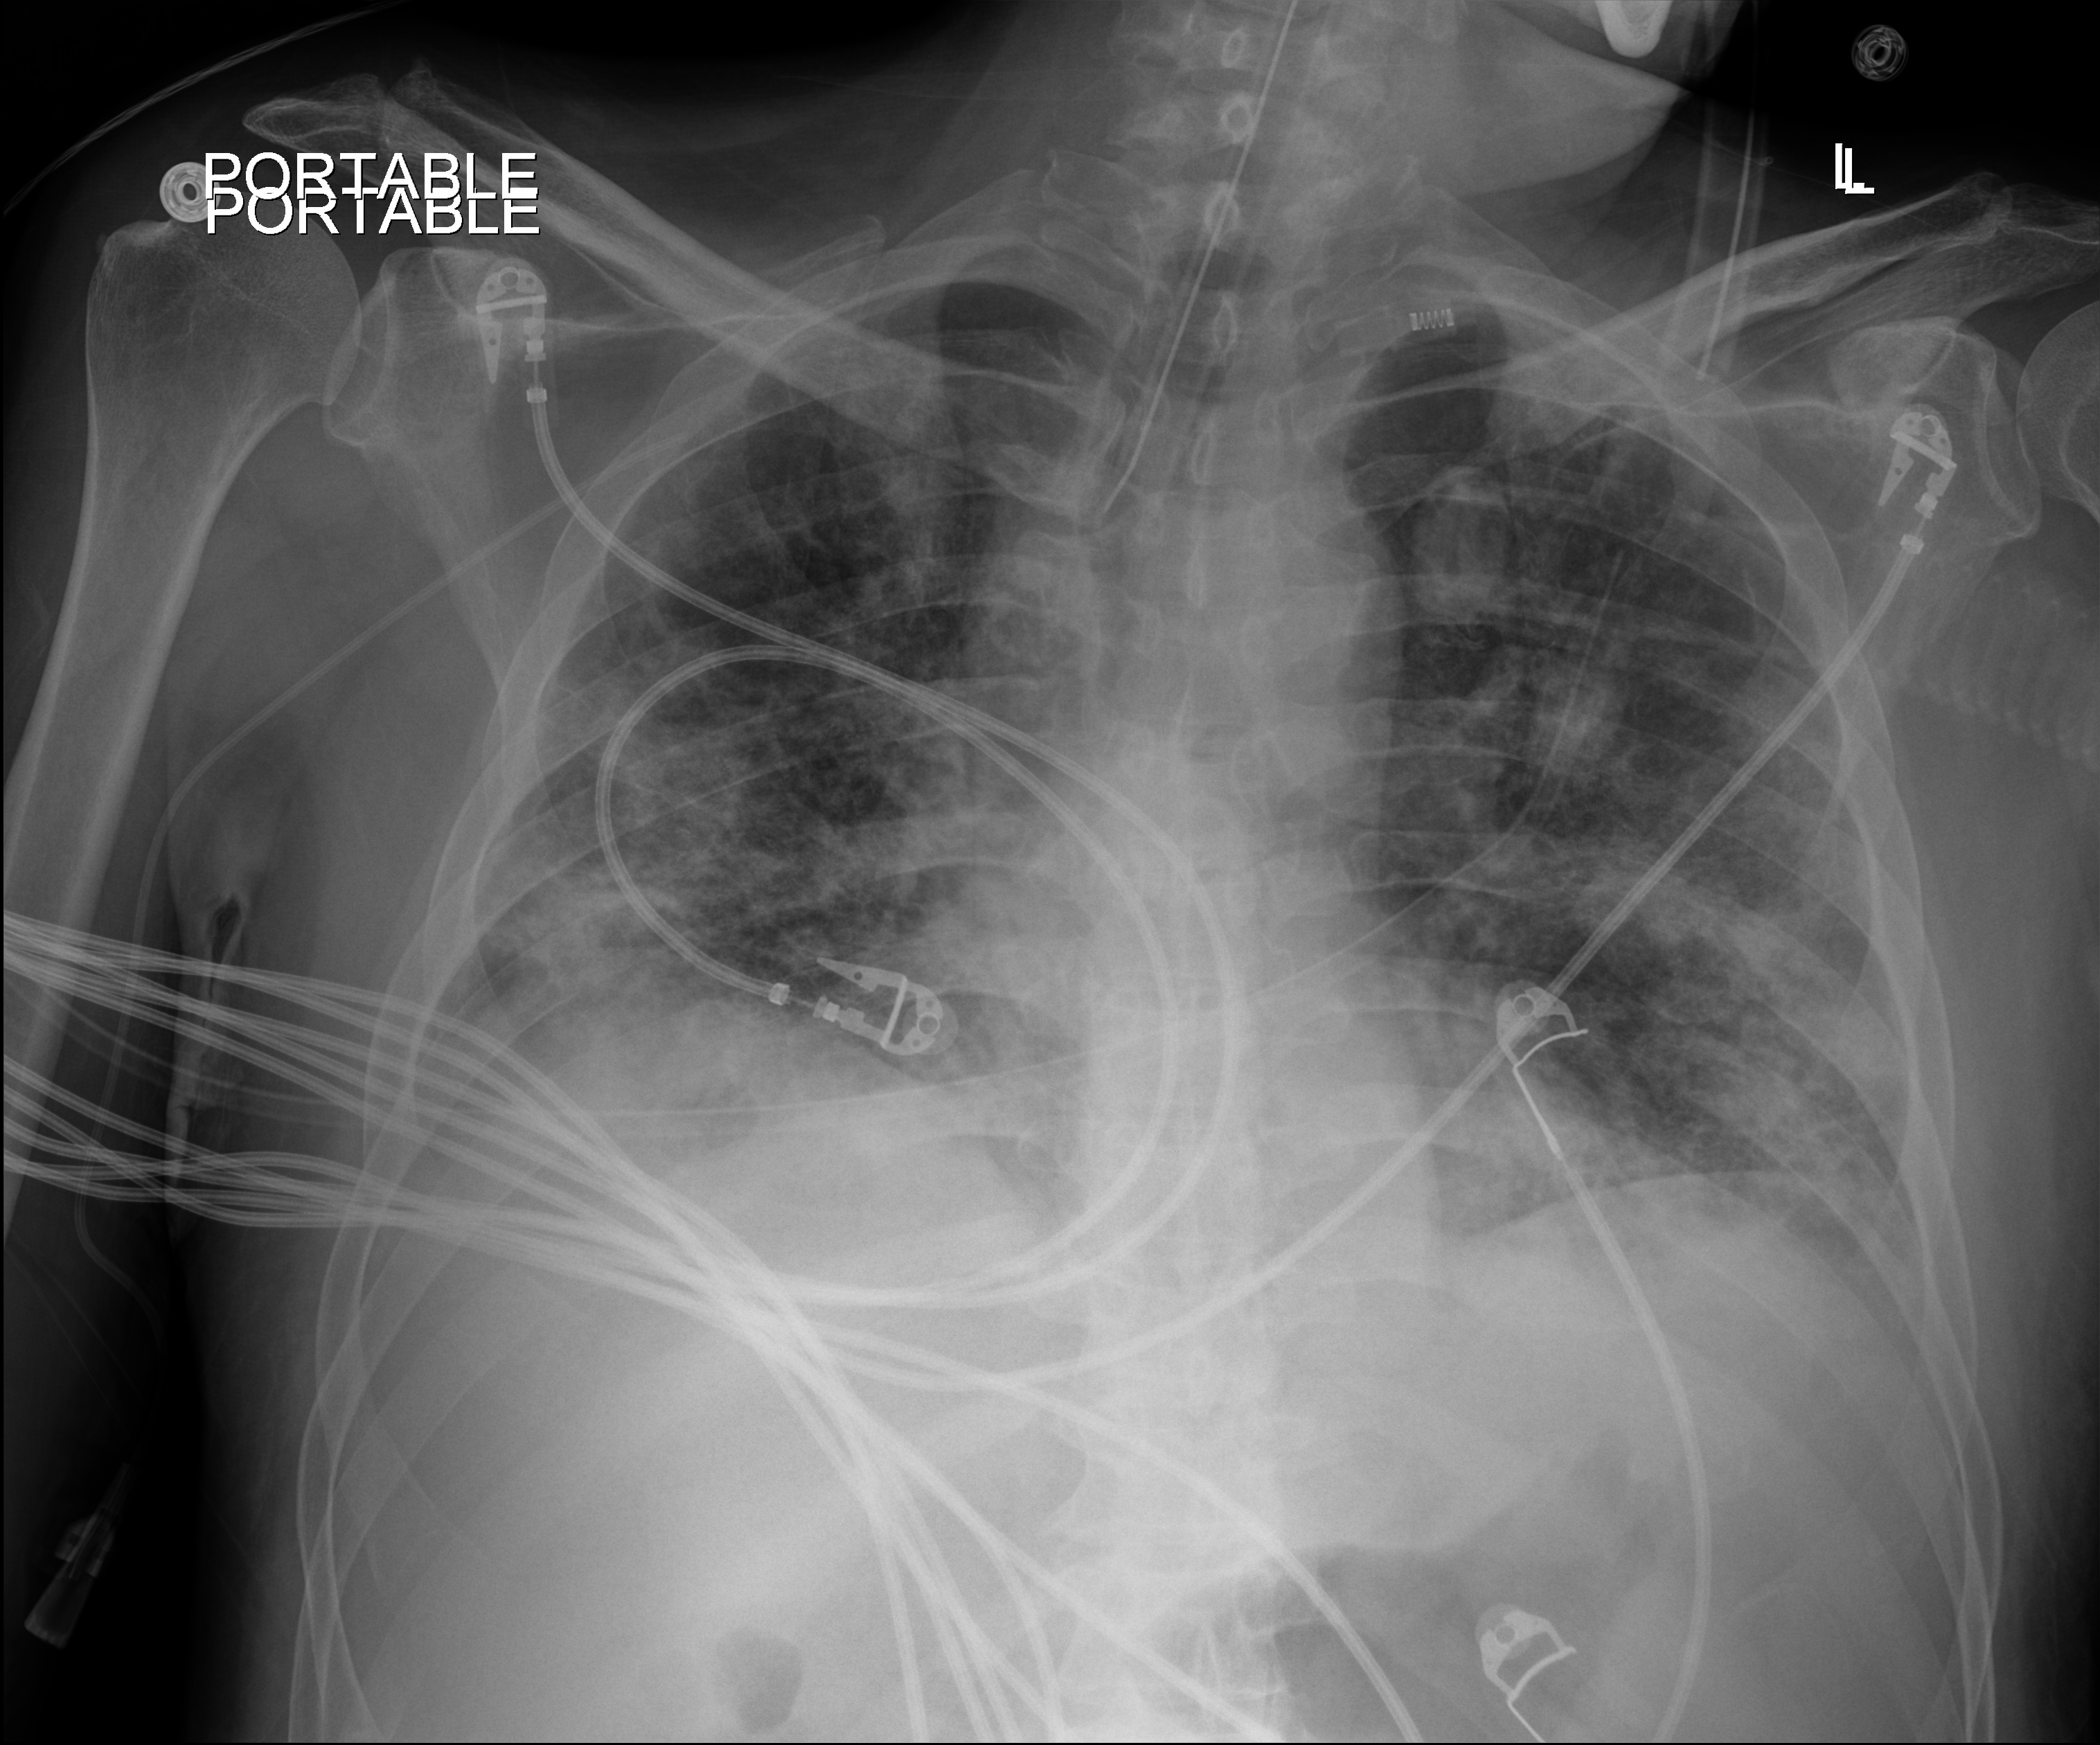
Portable chest radiograph; anteroposterior (AP) projection. Patient hospitalised with COVID-19; male, aged 18–59 years.
From the hospital-stay record, not from the radiograph (when in the stay this image was taken is not recorded): mechanically ventilated during this hospital stay: yes.